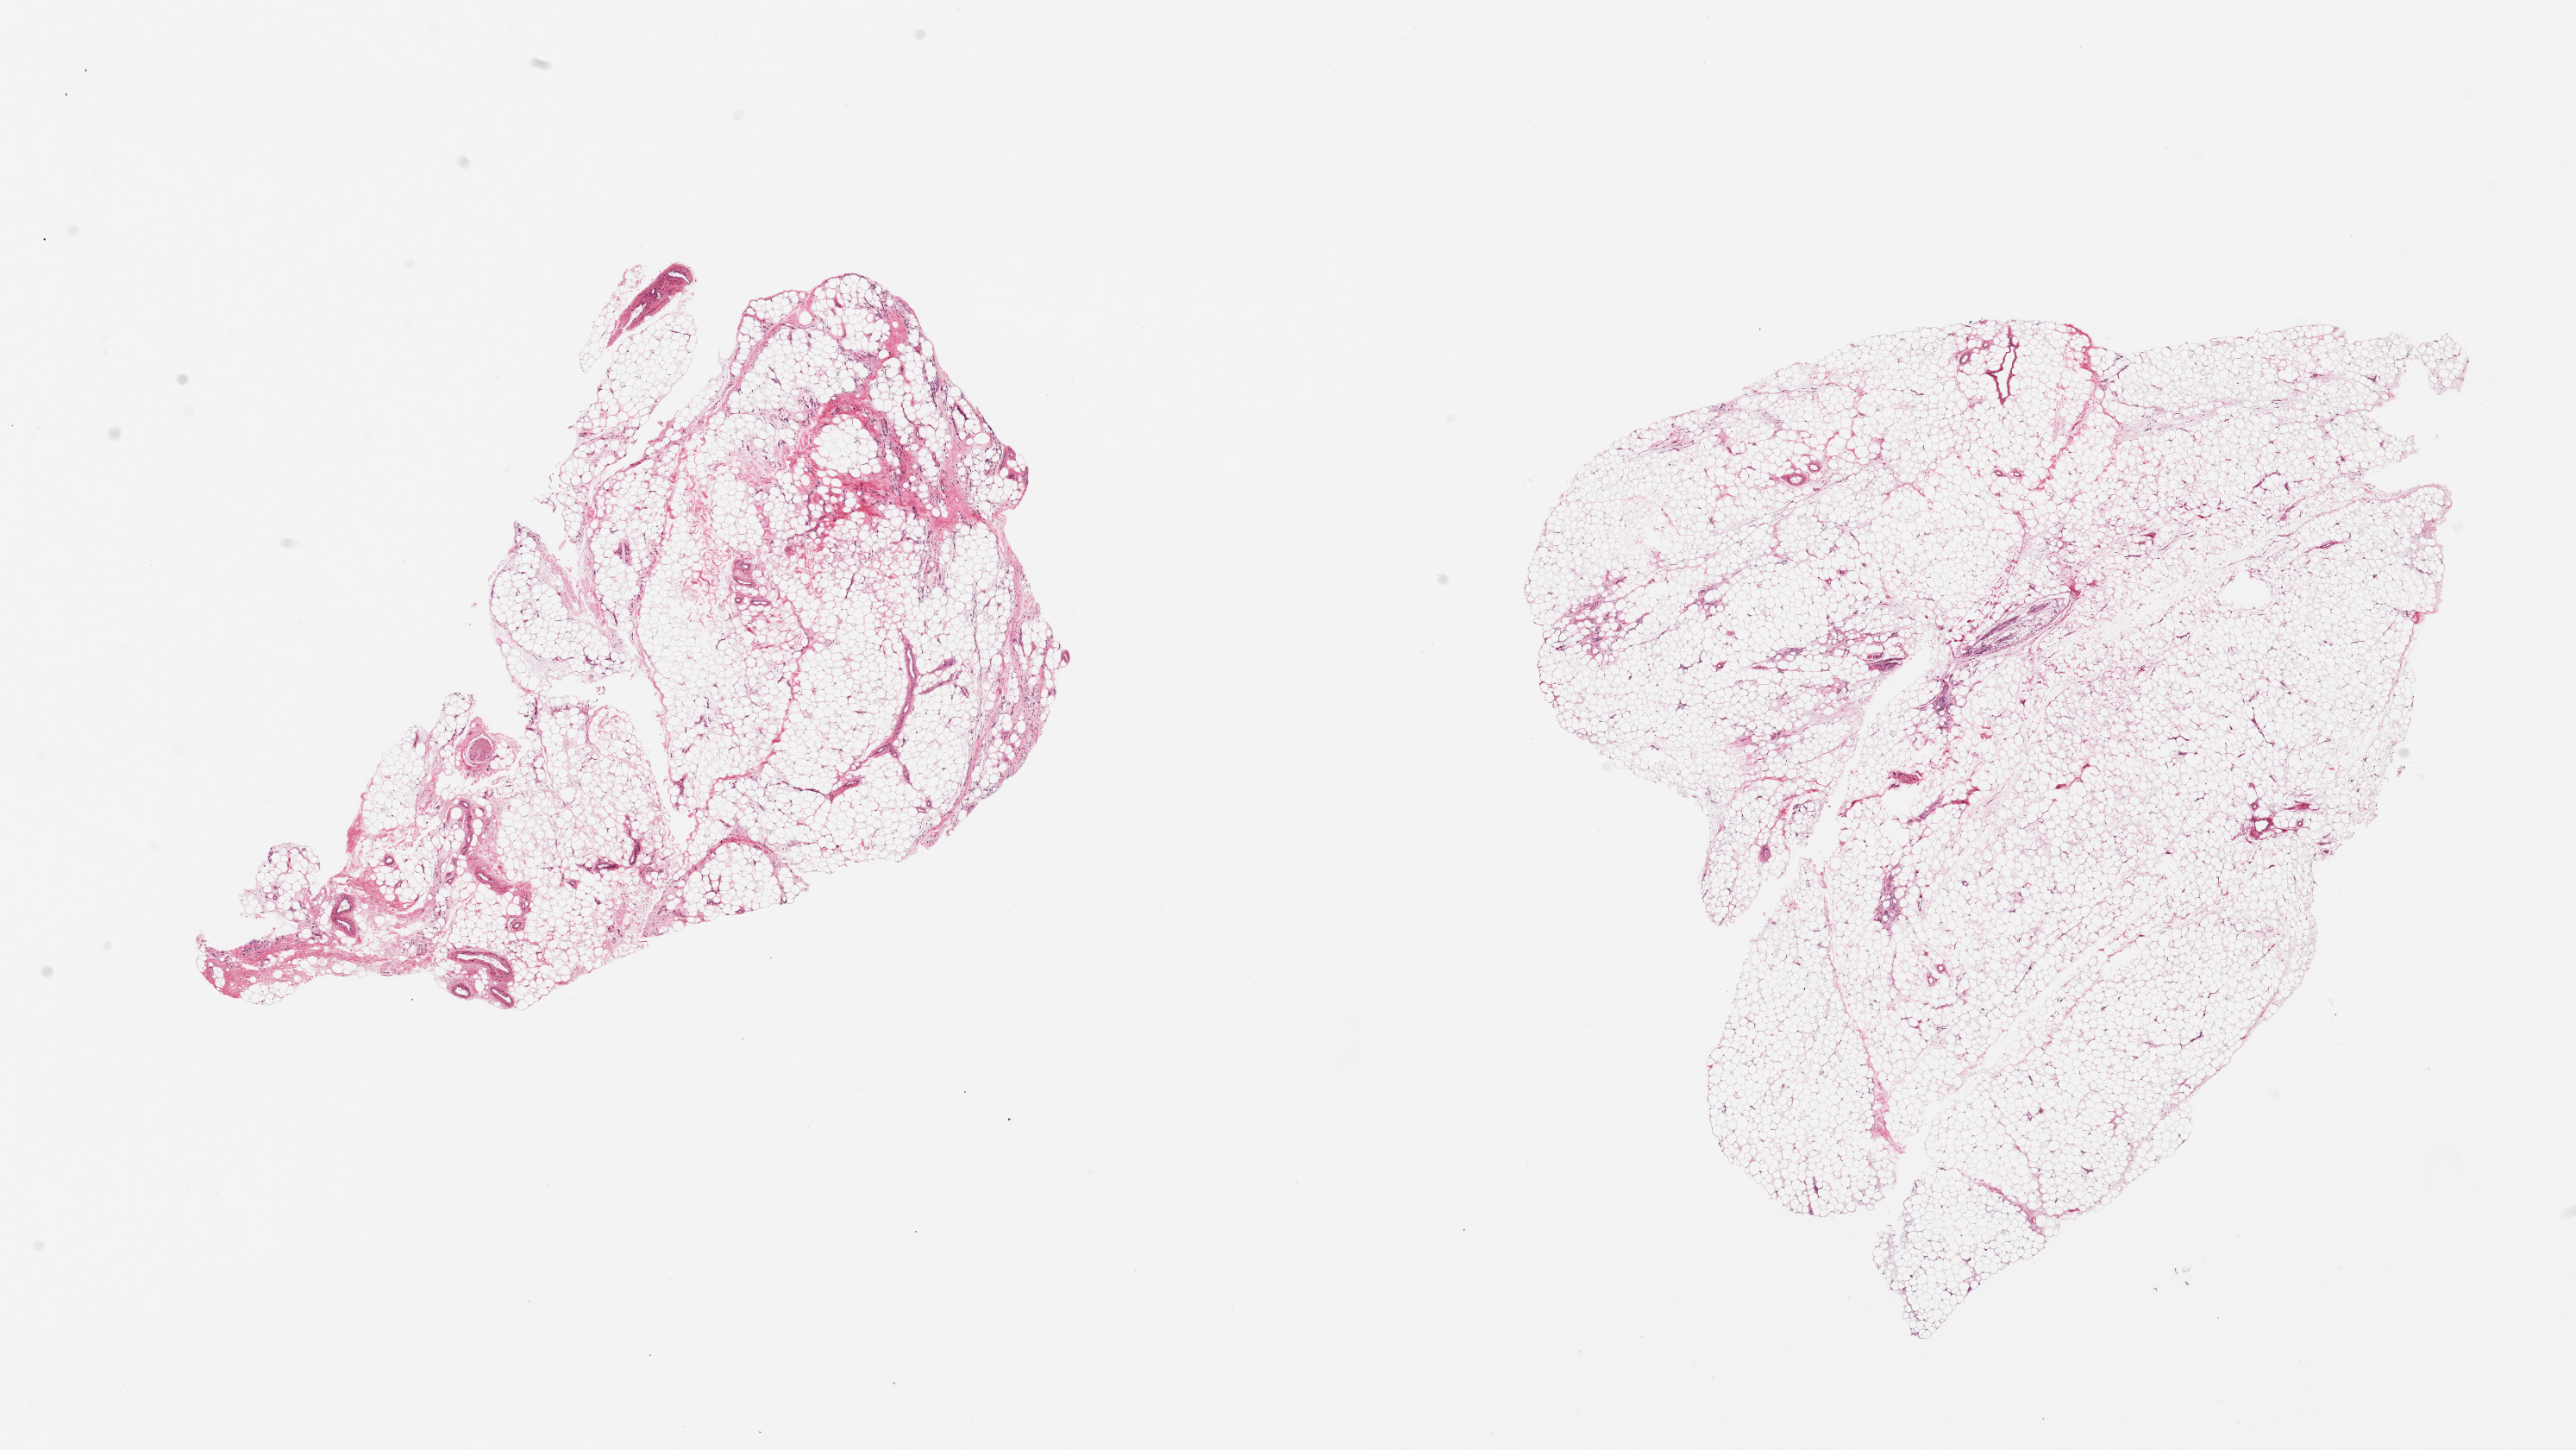
Hematoxylin and eosin (H&E) whole-slide image, shown as a low-resolution overview of the whole scanned area (about 23.6 x 13.3 mm, from a 20x scan), PAXgene-fixed, paraffin-embedded tissue, target tissue: skeletal muscle, tissue donor sample.
* review note (as recorded): 2 pieces; adipose tissue, not skeletal muscle